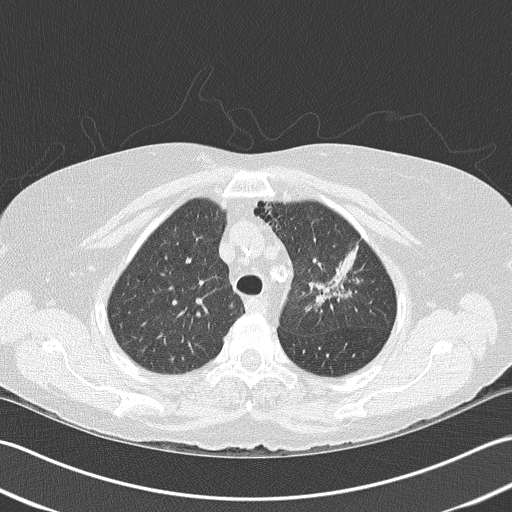
Chest CT (low-dose screening protocol), one axial image, baseline screening round, lung window (W 1500 / L -600 HU), 2 mm slice thickness, slice 124 of 159 in the series. Female, age 68 years at enrolment. Former smoker at enrolment.
Lesion marked by an expert reader, bounding box [x1, y1, x2, y2] px = [295, 233, 369, 315]. Screening reader's record for this exam: no non-calcified nodule ≥4 mm recorded. Official screen result: negative screen, minor abnormalities not suspicious for lung cancer.